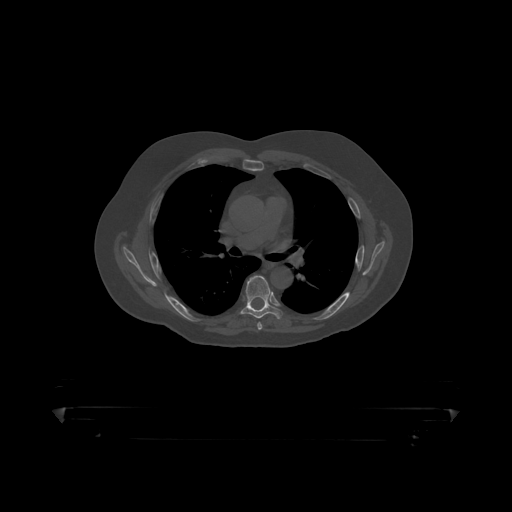
CT including the spine, one axial slice; slice 303 of 390 in the series (ordered by position); 120 kVp; bone window (W 1800 / L 400 HU); 1.25 mm slice thickness; 512 × 512 image matrix, field of view 650 × 650 mm. Male patient, age 60 years. Case-level facts recorded for this patient, not image findings: primary cancer: prostate.
Structures marked on this image (semi-automatically segmented with operator editing):
- T6 vertebra: bounding box [x1, y1, x2, y2] px = [241, 276, 282, 319]